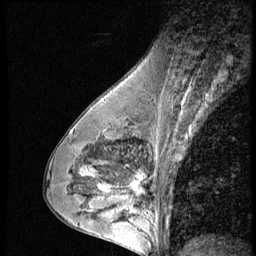
Breast MRI (dynamic contrast-enhanced), one sagittal slice. 3 images stored at this slice position (order not interpretable as contrast timing). 1.5 T. TE 4.2 ms, TR 9 ms. 2.5 mm slice thickness. 256 × 256 image matrix, field of view 180 × 180 mm. Female patient, age 43 years. Case-level facts recorded for this patient, not image findings: setting: breast cancer imaged before/during neoadjuvant chemotherapy; receptor status: HR-positive, HER2-negative.
Annotated regions visible in this slice (semi-automatic segmentation, software-assisted and operator-edited):
- analysis volume of interest (the breast-tissue region the enhancement analysis was run in; not a lesion): box from (x=120, y=160) to (x=163, y=207) px
- tumour enhancement mask (voxels above the 140 % enhancement threshold inside the analysis volume of interest): (x=125, y=174)–(x=147, y=197)